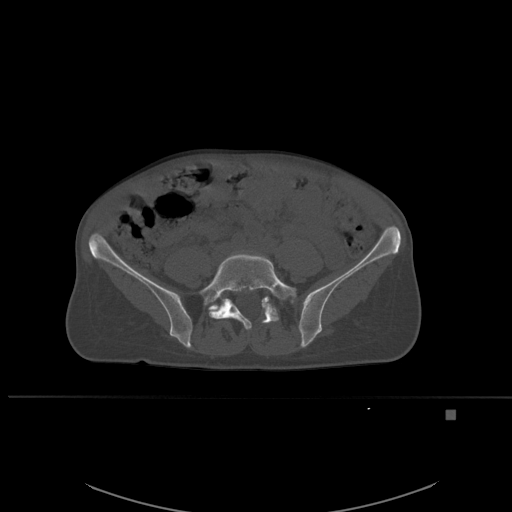
CT including the spine, one axial slice. Position 172 of 537 along the scan axis. Bone window (W 1800 / L 400 HU). 1.5 mm slice thickness. 512 × 512 image matrix. Patient: female, 45 years. Case-level facts recorded for this patient, not image findings: primary cancer: lung.
Annotated regions visible in this slice (semi-automatic segmentation, software-assisted and operator-edited):
- L5 vertebra: box from (x=199, y=253) to (x=297, y=330) px